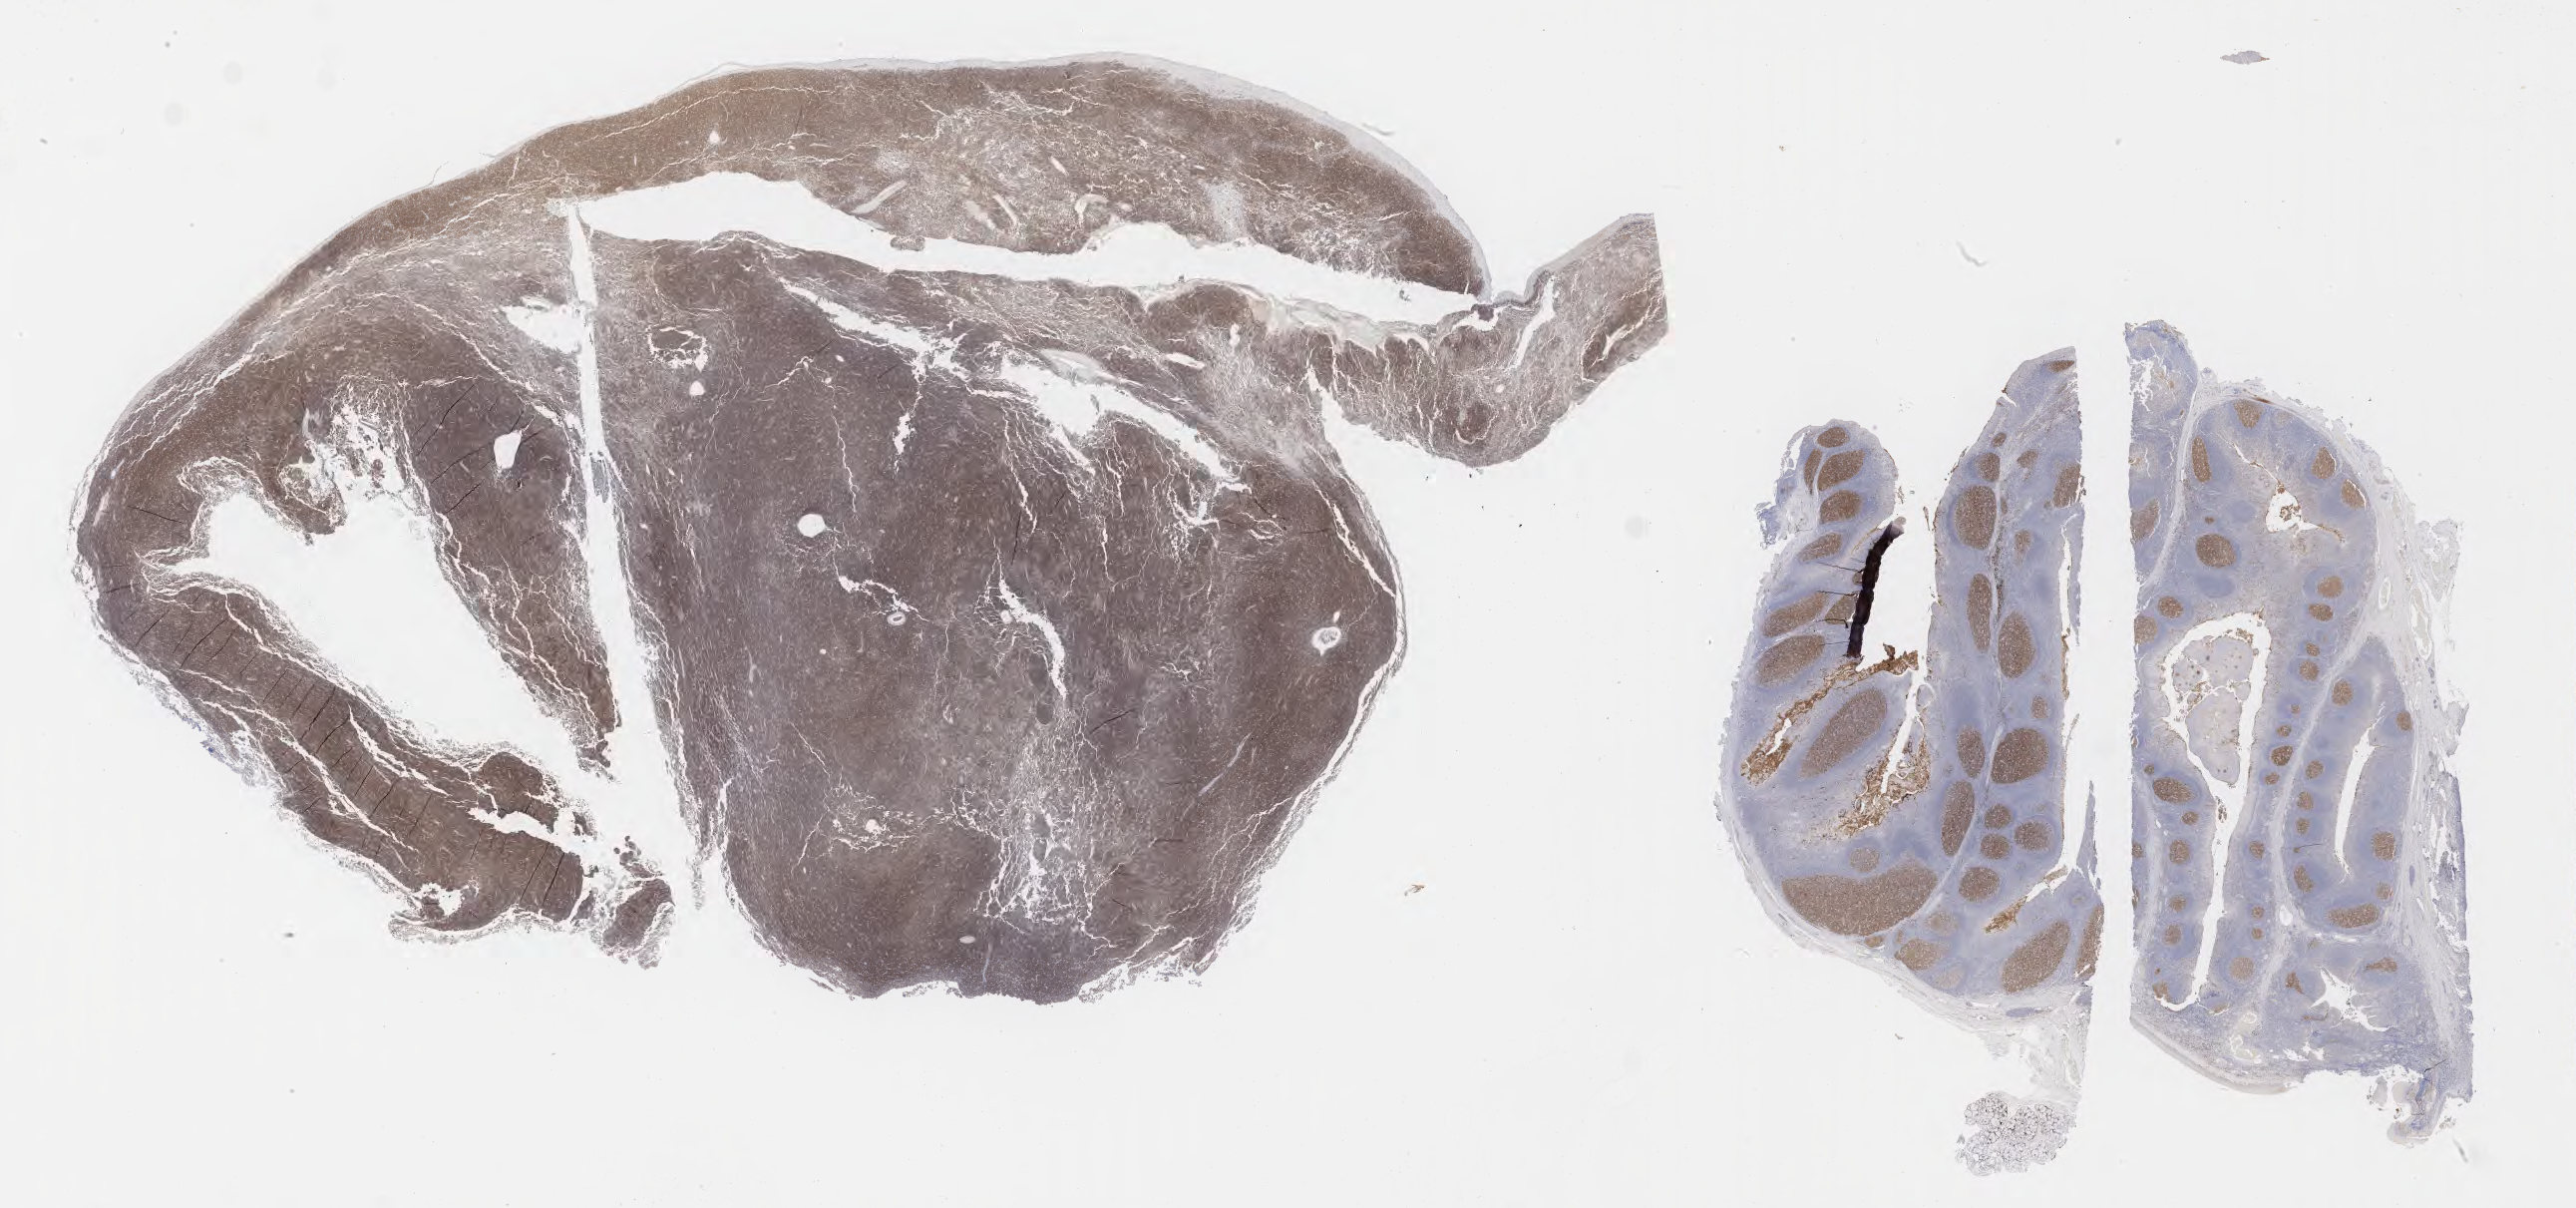
Immunohistochemistry (IHC) whole-slide image stained for CD10 — shown as a low-resolution overview of the whole scanned area (about 41.8 x 19.6 mm); specimen: tumor tissue. Patient: female, age at initial diagnosis 3 years.
• diagnosis: Burkitt lymphoma, NOS